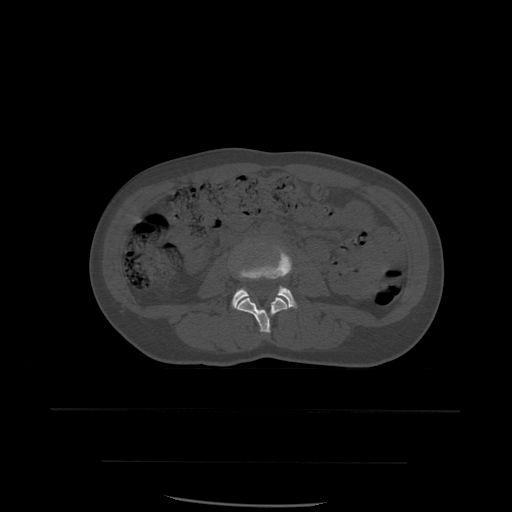
CT including the spine, one axial slice. Slice 185 of 574 in the series (ordered by position). Bone window (W 1800 / L 400 HU). 1.25 mm slice thickness. 512 × 512 image matrix, field of view 392 × 392 mm. Patient age 48 years. From the clinical record (not read from this slice): primary cancer: lung.
Structures marked on this image (semi-automatic segmentation, software-assisted and operator-edited):
- L3 vertebra: bounding box <236,297,288,333> (left, top, right, bottom; pixels)
- L4 vertebra: <232,249,297,308>